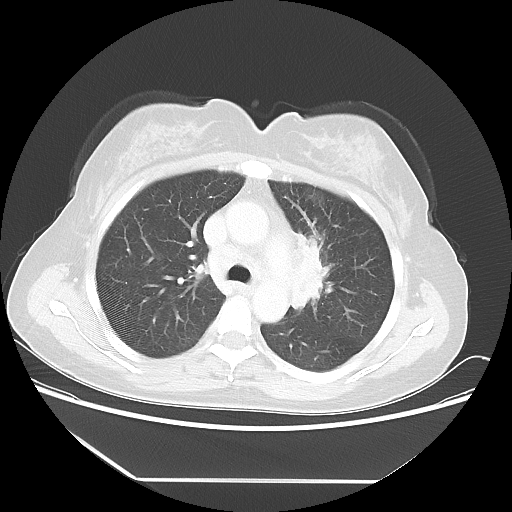
Chest CT, one axial slice; slice 35 of 52 in the series (ordered by position); reconstruction kernel LUNG; 100 kVp; lung window (W 1500 / L -600 HU); 5 mm slice thickness; 512 × 512 image matrix. Patient: female, 50 years. From the clinical record (not read from this slice): clinical TNM (as recorded): T2 N3 M0.
Structures marked on this image (rectangle marked by the reading radiologist):
- lung tumour (recorded histology: adenocarcinoma): bounding box [x1, y1, x2, y2] px = [284, 224, 345, 324]